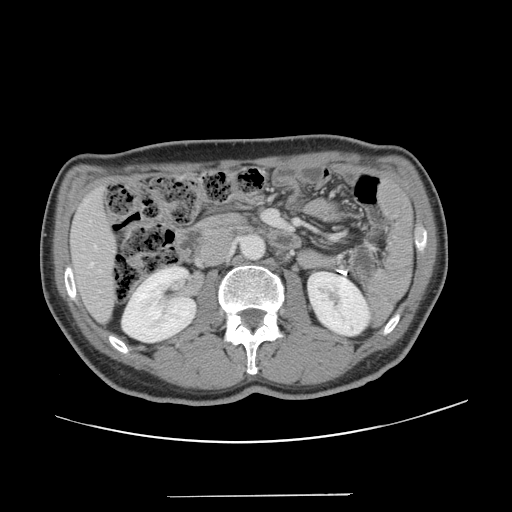
Contrast-enhanced abdominal CT, one axial slice; slice 55 of 131 in the series (ordered by position); intravenous contrast given; soft-tissue window (W 400 / L 40 HU); 2.5 mm slice thickness; 512 × 512 image matrix, field of view 403 × 403 mm. Male patient, age 60 years. From the clinical record (not read from this slice): diagnosis: colorectal cancer liver metastases, imaged before liver resection; multiple liver metastases: no; largest metastasis: 2.5 cm.
Outlined on this slice (outlined manually by an expert reader):
- hepatic veins: bounding box <91,246,96,266> (left, top, right, bottom; pixels)
- liver: <71,193,115,319>
- planned liver remnant (the part of the liver to remain after resection): <71,193,115,320>